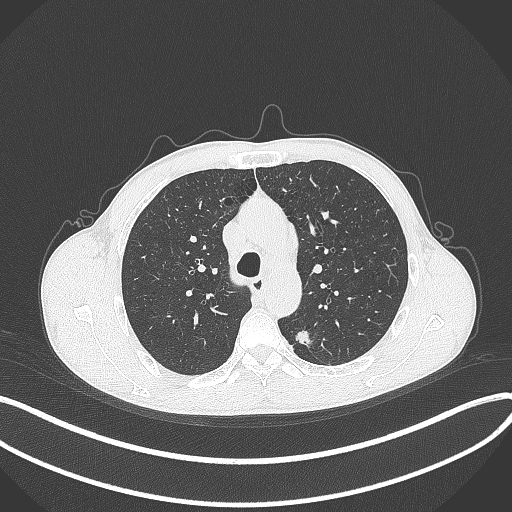
Chest CT, one axial slice; position 280 of 429 along the scan axis; reconstruction kernel B70f; 120 kVp; lung window (W 1500 / L -600 HU); 1 mm slice thickness; 512 × 512 image matrix, field of view 400 × 400 mm. Patient: male, 51 years. Case-level facts recorded for this patient, not image findings: clinical TNM (as recorded): T2a N1 M1.
Outlined on this slice (bounding box drawn by a radiologist):
- lung tumour (recorded histology: adenocarcinoma): bounding box [x1, y1, x2, y2] px = [293, 327, 319, 353]